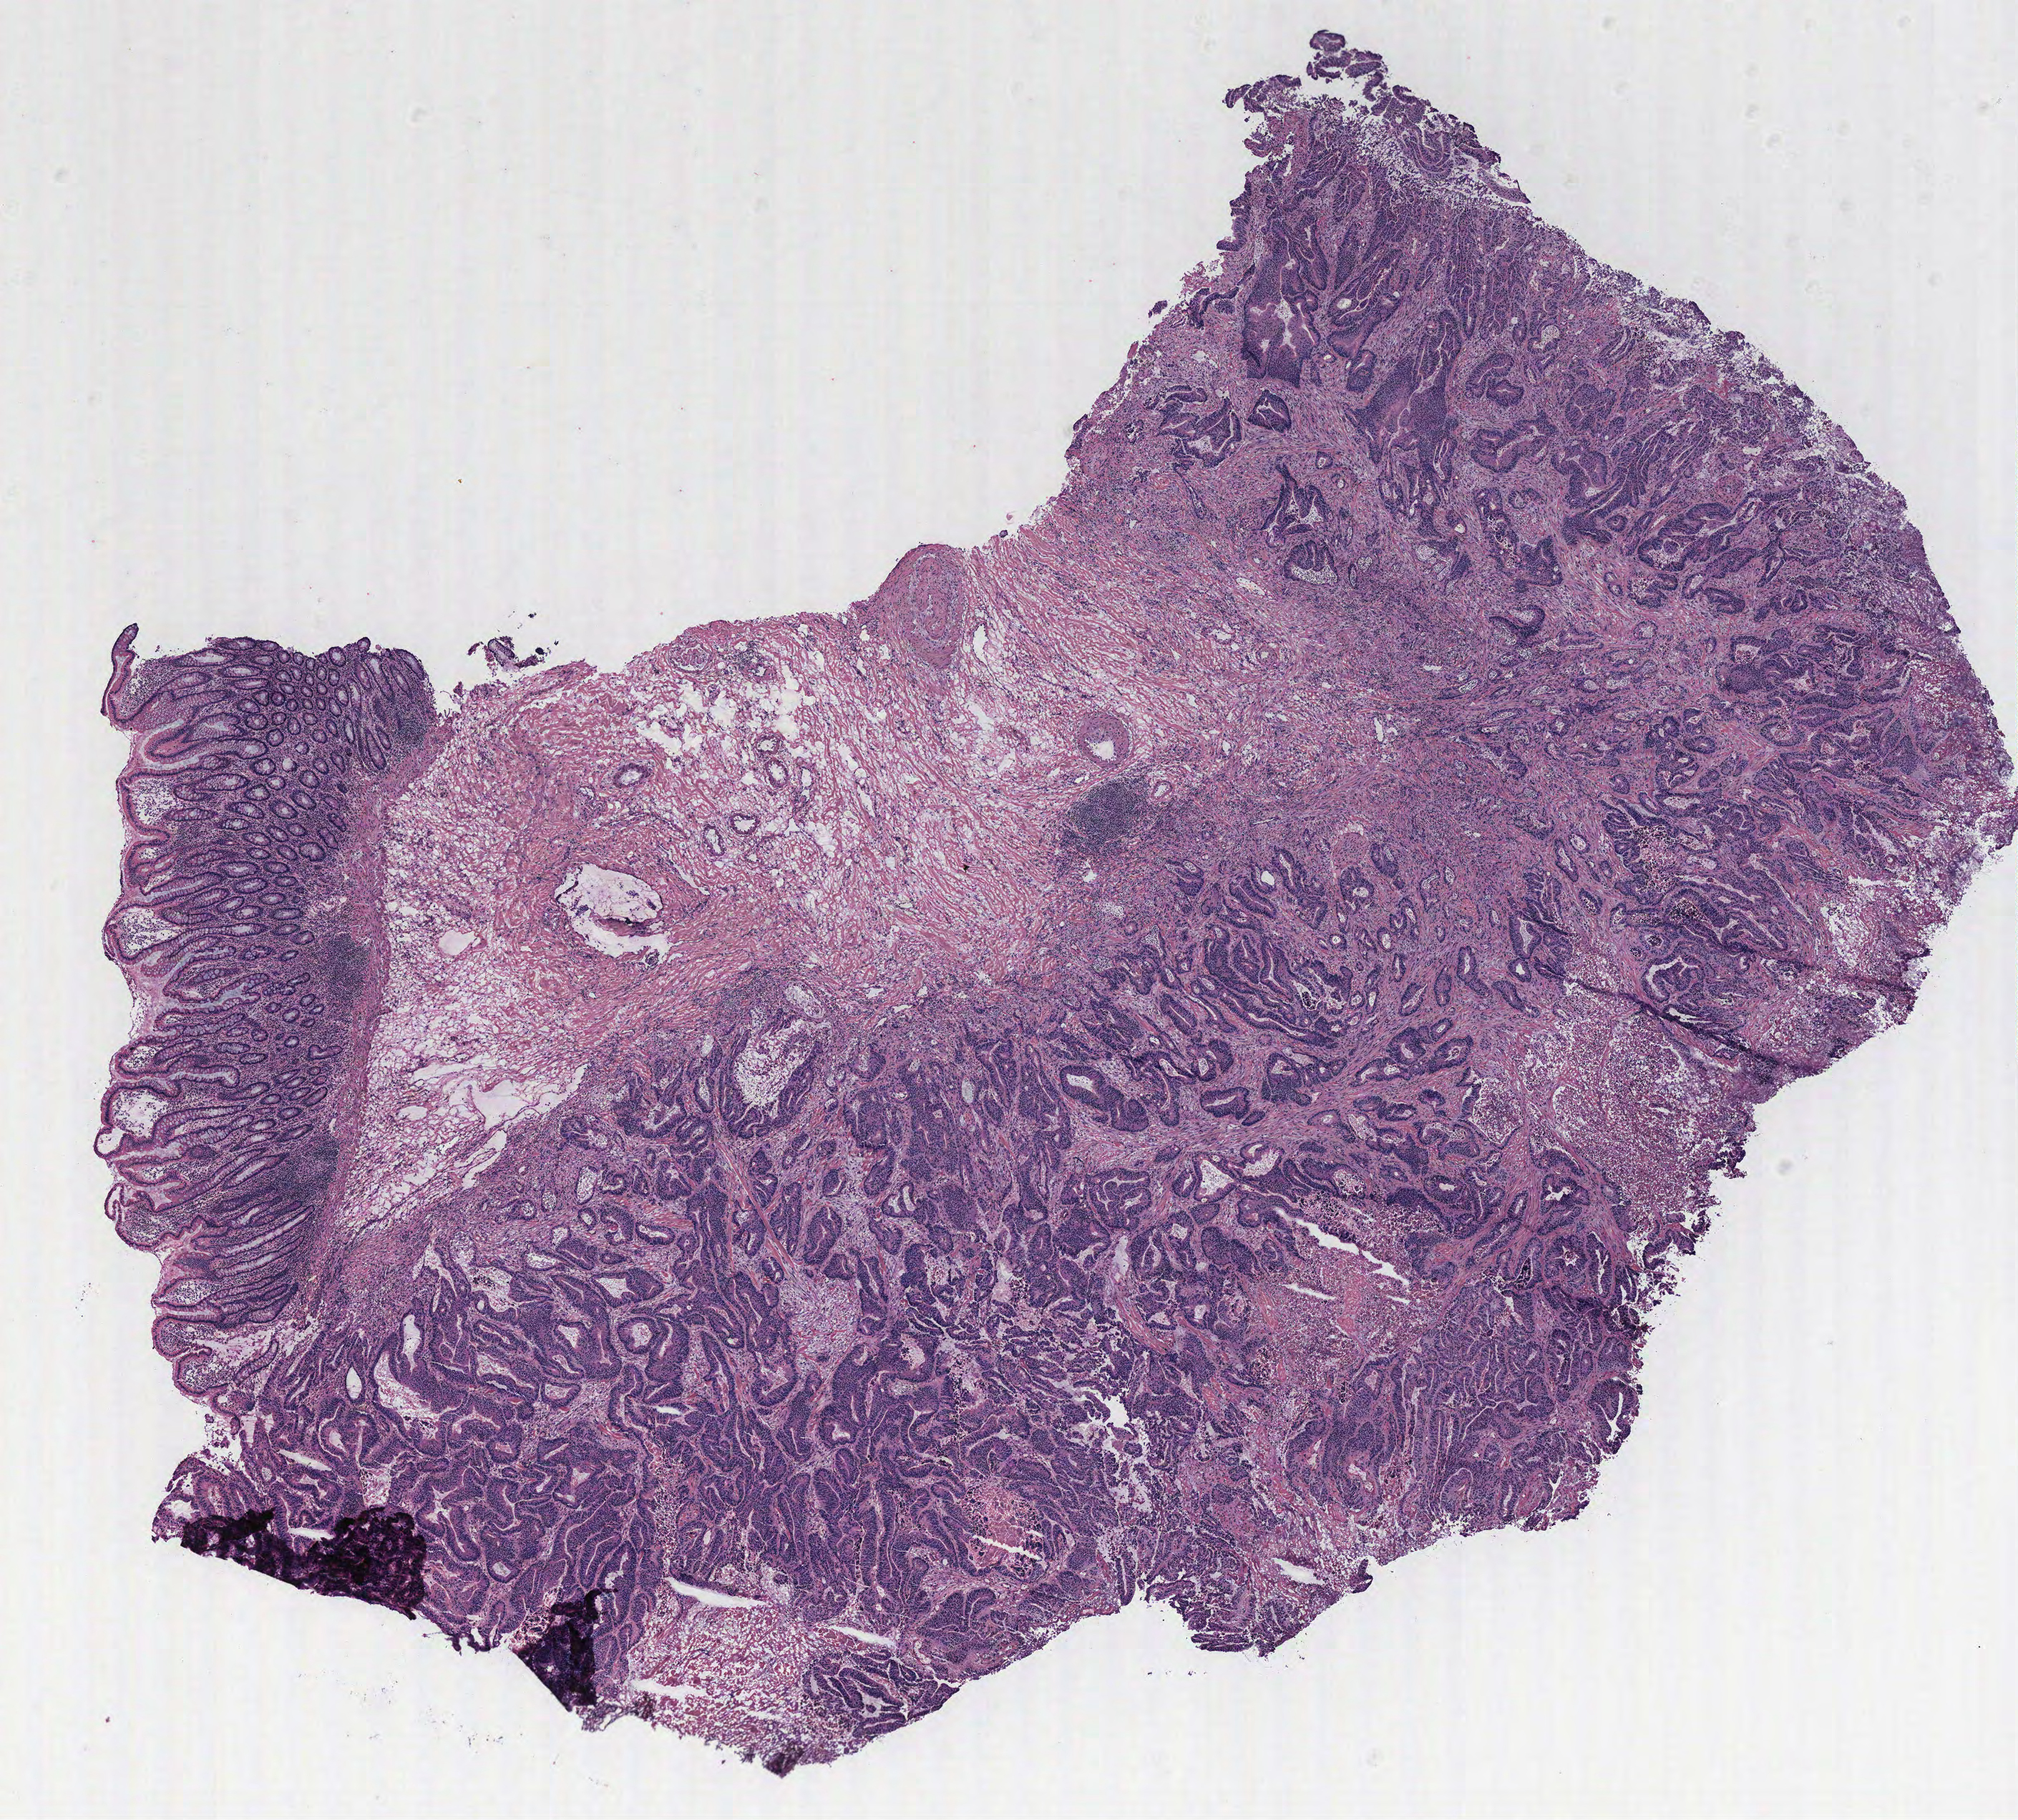
Whole-slide histology image, H&E — whole scanned area (about 11.3 x 10.2 mm) shown as a low-resolution overview, colon, normal (non-tumour) tissue. Male, 58 y/o.
This section: normal (non-tumour) tissue from the same patient. Patient diagnosis (cohort enrolment): colon cancer (colon).